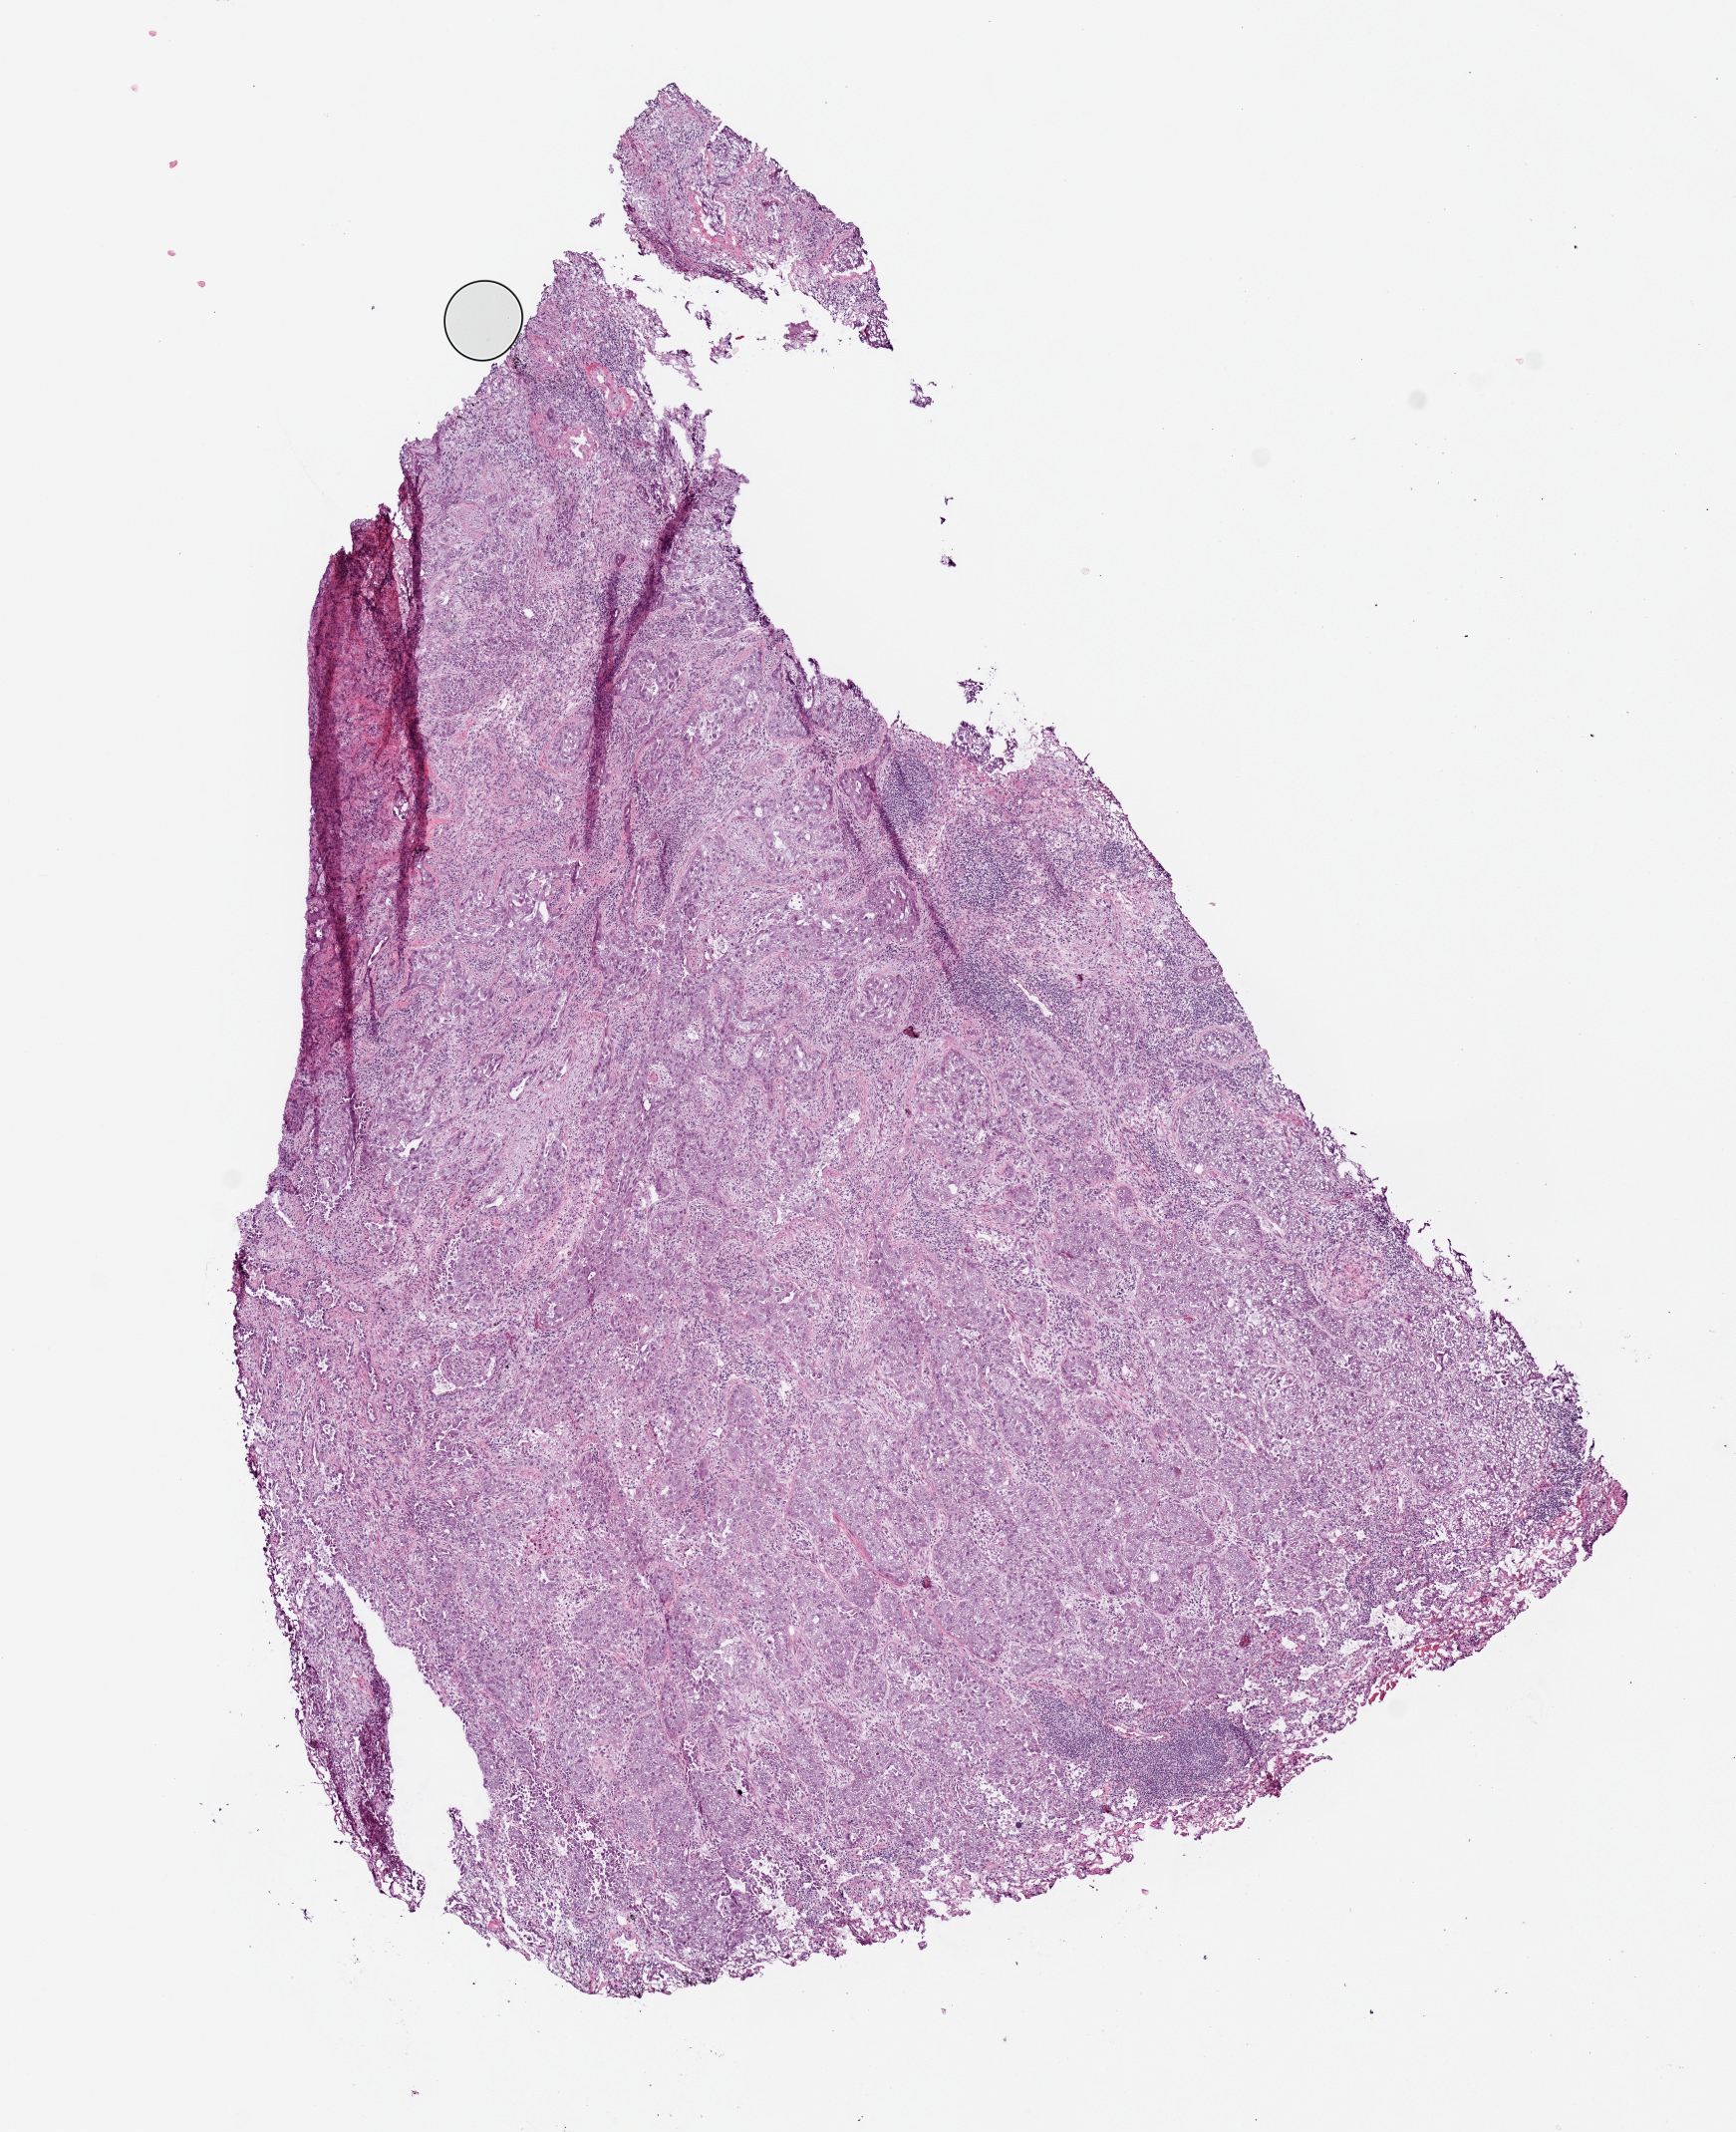
Whole-slide histology image, Hematoxylin and eosin (H&E) stained, whole scanned area (about 6.9 x 8.5 mm) shown as a low-resolution overview. Frozen section. Primary tumour sample from the lung. Female patient; age at initial diagnosis 53 years. Composition of this section per pathologist review: tumour cells 100%, tumour nuclei 60%.
Histologic diagnosis: Adenocarcinoma, NOS (upper lobe, lung).